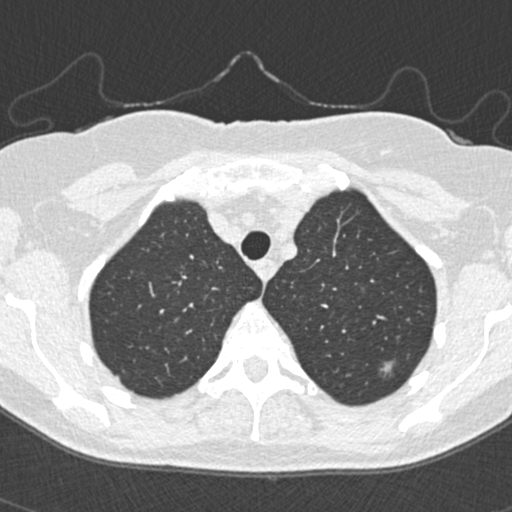
Low-dose screening chest CT, one axial slice; slice 299 of 350 in the series (ordered by position); reconstruction kernel B30f; 120 kVp; lung window (W 1500 / L -600 HU); 1 mm slice thickness; 512 × 512 image matrix, field of view 298 × 298 mm.
Structures marked on this image (manually delineated by an expert):
- lesion 2 (tumor, upper lobe of left lung): bounding box (x1, y1, x2, y2) in pixels: (382, 361, 394, 373)